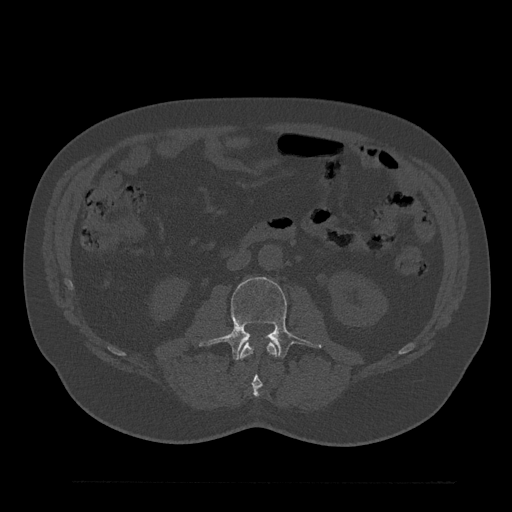
CT including the spine, one axial slice. Position 53 of 797 along the scan axis. 120 kVp. Bone window (W 1800 / L 400 HU). 512 × 512 image matrix, field of view 430 × 430 mm. Male patient, age 61 years. From the clinical record (not read from this slice): primary cancer: prostate.
Annotated regions visible in this slice (semi-automatically segmented with operator editing):
- L2 vertebra: bounding box [x1, y1, x2, y2] px = [239, 342, 278, 398]
- L3 vertebra: [200, 277, 321, 360]